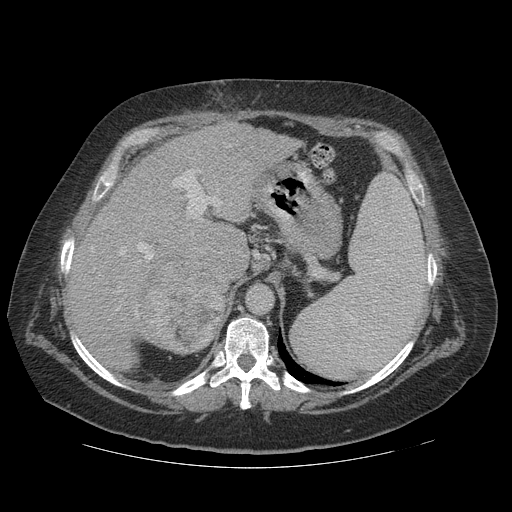
Contrast-enhanced abdominal CT (liver protocol), one axial slice. Slice 82 of 121 in the series (ordered by position). Reconstruction kernel STANDARD. Soft-tissue window (W 400 / L 40 HU). 2.5 mm slice thickness. 512 × 512 image matrix. Case-level facts recorded for this patient, not image findings: diagnosis: hepatocellular carcinoma (patient treated with transarterial chemoembolisation; whether this scan precedes or follows treatment is not stated here); TNM stage (as recorded): Stage-IIIA; Child-Pugh class: A; tumour differentiation: well differentiated.
Annotated regions visible in this slice (semi-automatic segmentation, software-assisted and operator-edited):
- liver parenchyma outside the tumour (the mass and vessels are separate outlines, so this box may not span the whole liver): bounding box <66,122,302,360> (left, top, right, bottom; pixels)
- mass: <133,250,226,355>
- liver vessels: <91,145,245,311>